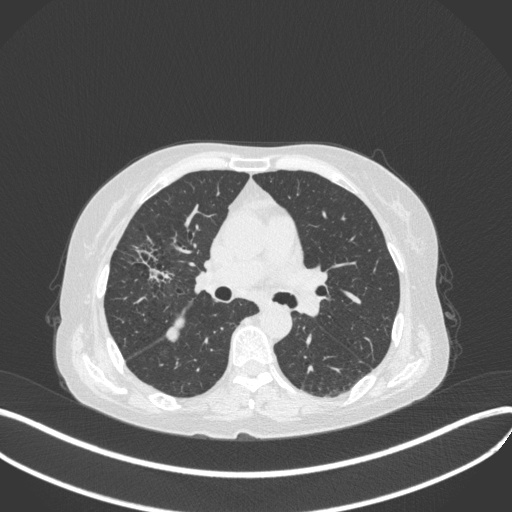
Chest CT, one axial slice; slice 233 of 429 in the series (ordered by position); lung window (W 1500 / L -600 HU); 1 mm slice thickness; 512 × 512 image matrix, field of view 400 × 400 mm. Female patient, age 69 years. Case-level facts recorded for this patient, not image findings: clinical TNM (as recorded): T1b N3 M0.
Outlined on this slice (bounding box drawn by a radiologist):
- lung tumour (recorded histology: small cell carcinoma): bounding box (x1, y1, x2, y2) in pixels: (124, 235, 175, 288)